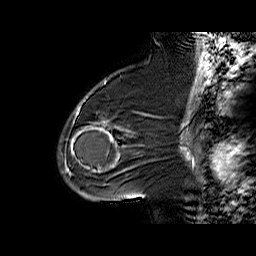
Breast MRI (dynamic contrast-enhanced), one sagittal slice; slice 40 of 60 in the series (ordered by position); dynamic contrast-enhanced series, time point 2 of 6 at this slice position (early post-contrast); 1.5 T; TE 6.3 ms, TR 32.4 ms; 4 mm slice thickness; 256 × 256 image matrix. Female patient. Case-level facts recorded for this patient, not image findings: setting: breast cancer imaged before/during neoadjuvant chemotherapy; receptor status: triple-negative.
Annotated regions visible in this slice (semi-automatically segmented with operator editing):
- analysis volume of interest (the breast-tissue region the enhancement analysis was run in; not a lesion): box from (x=65, y=88) to (x=140, y=187) px
- tumour enhancement mask (voxels above the 100 % enhancement threshold inside the analysis volume of interest): (x=70, y=121)–(x=128, y=172)